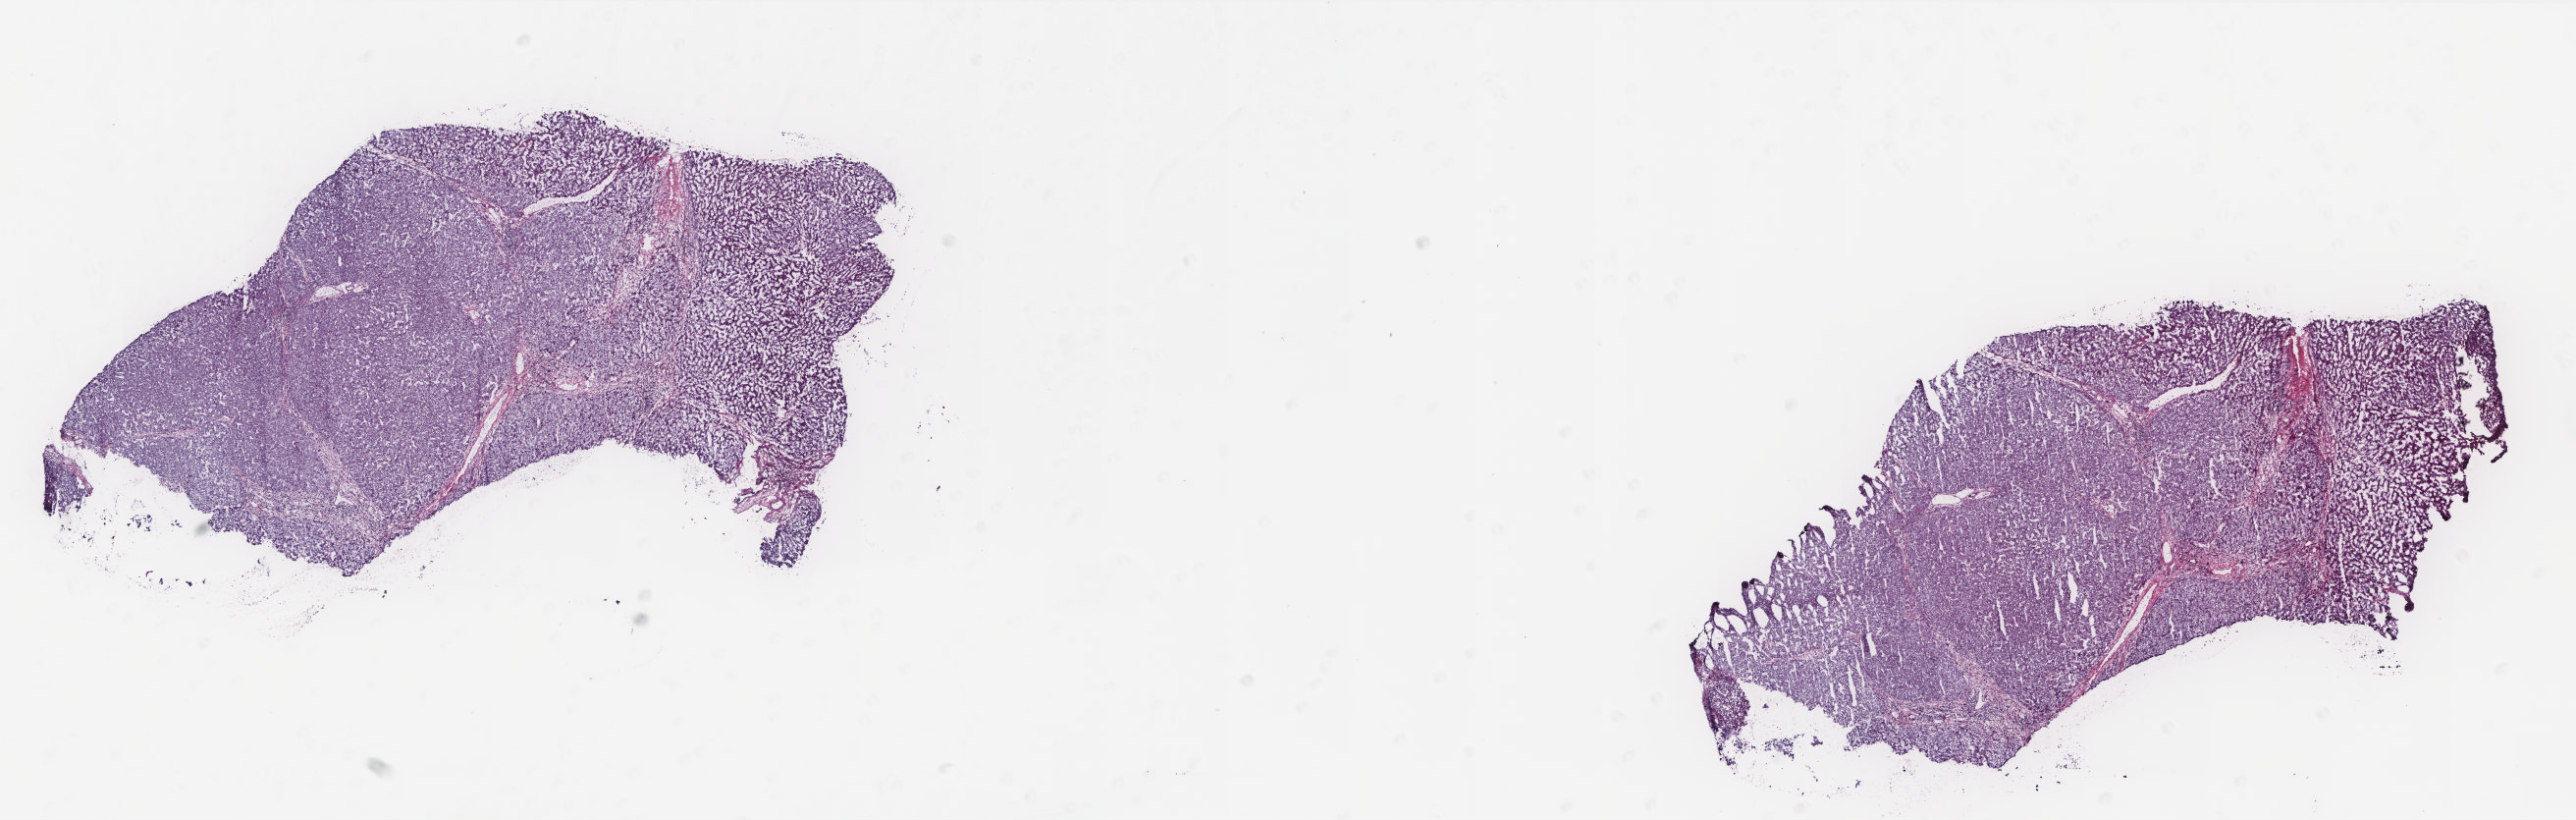
Whole-slide histology image, H&E-stained, shown as a low-resolution overview of the whole scanned area (about 21.0 x 6.7 mm, from a 20x scan). Frozen section. Sample: solid tissue normal (non-tumour tissue), liver. Male, age 62 years at initial diagnosis. Pathologist review of this section (percent, as recorded): tumour cells 0%, tumour nuclei 0%, normal cells 95%, stromal cells 5%, necrosis 0%. Infiltration values recorded for this section: lymphocyte infiltration 3%, monocyte infiltration 1%, neutrophil infiltration 0%.
This section: solid tissue normal (non-tumour) sample from the same patient. Patient diagnosis: Hepatocellular carcinoma, NOS.